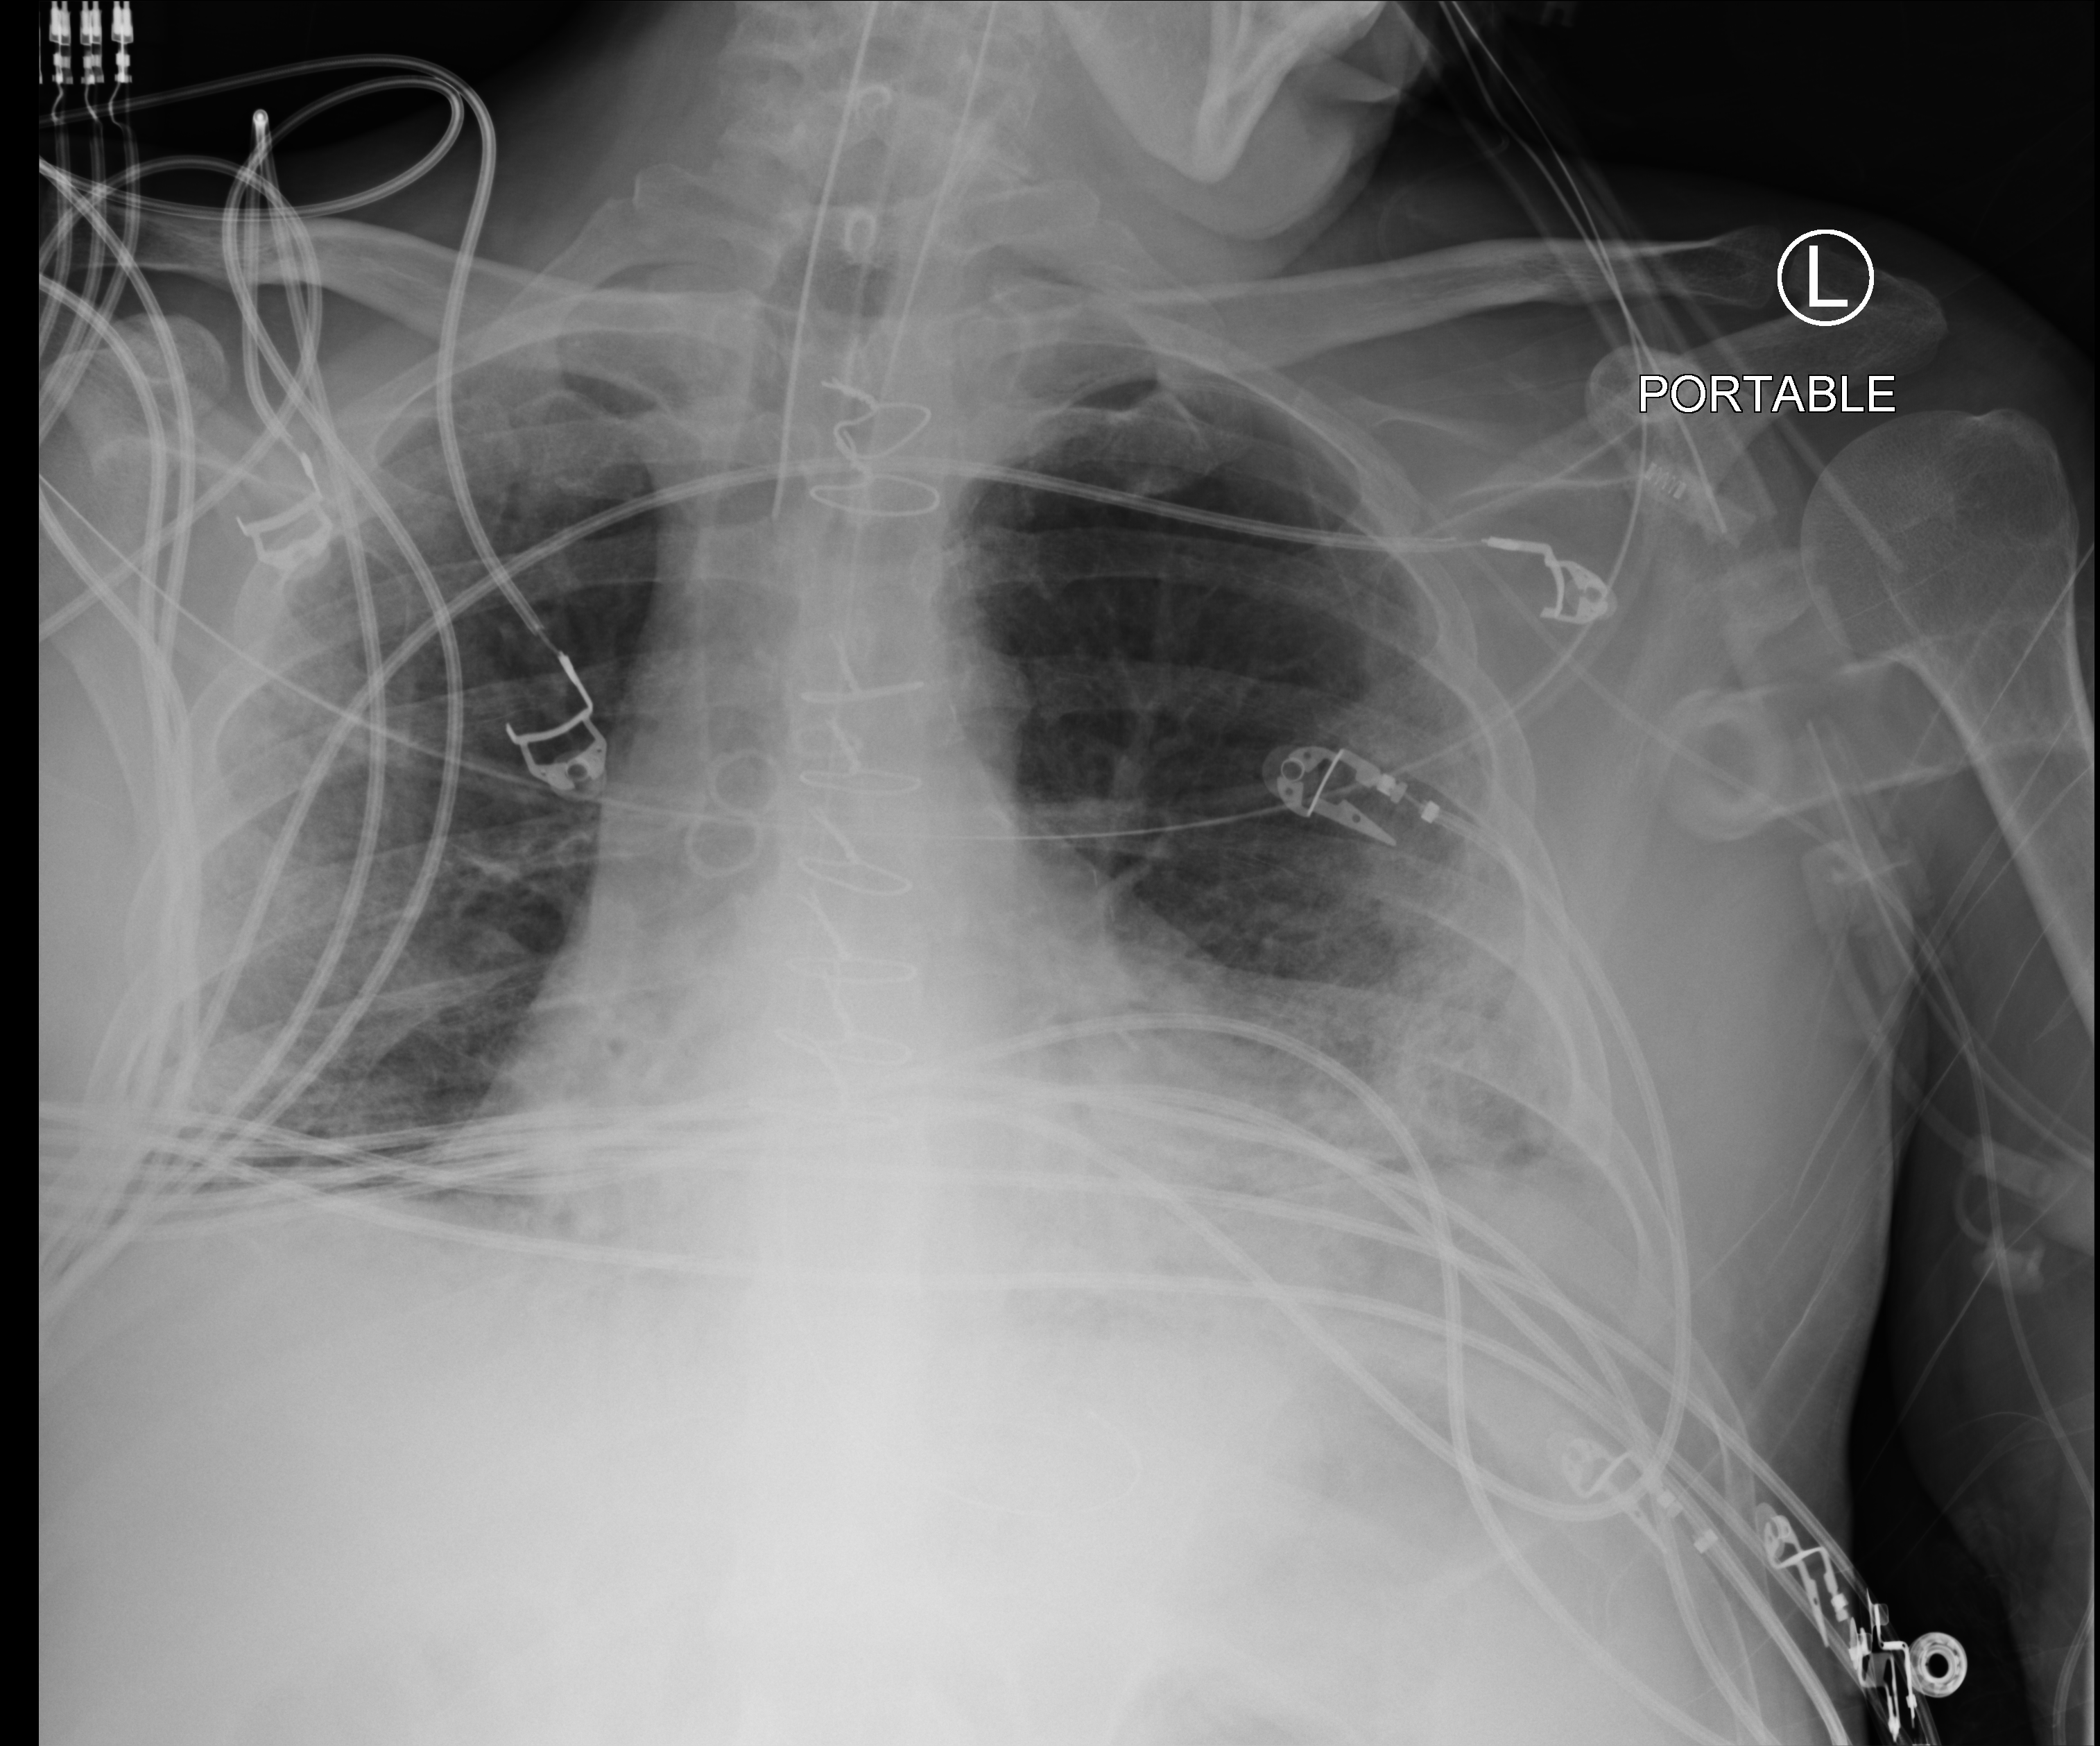
Bedside chest radiograph (computed radiography), anteroposterior (AP) projection. Male patient hospitalised with COVID-19, age 18–59 years.
From the hospital-stay record, not from the radiograph (when in the stay this image was taken is not recorded): hypertension (admission record): no.